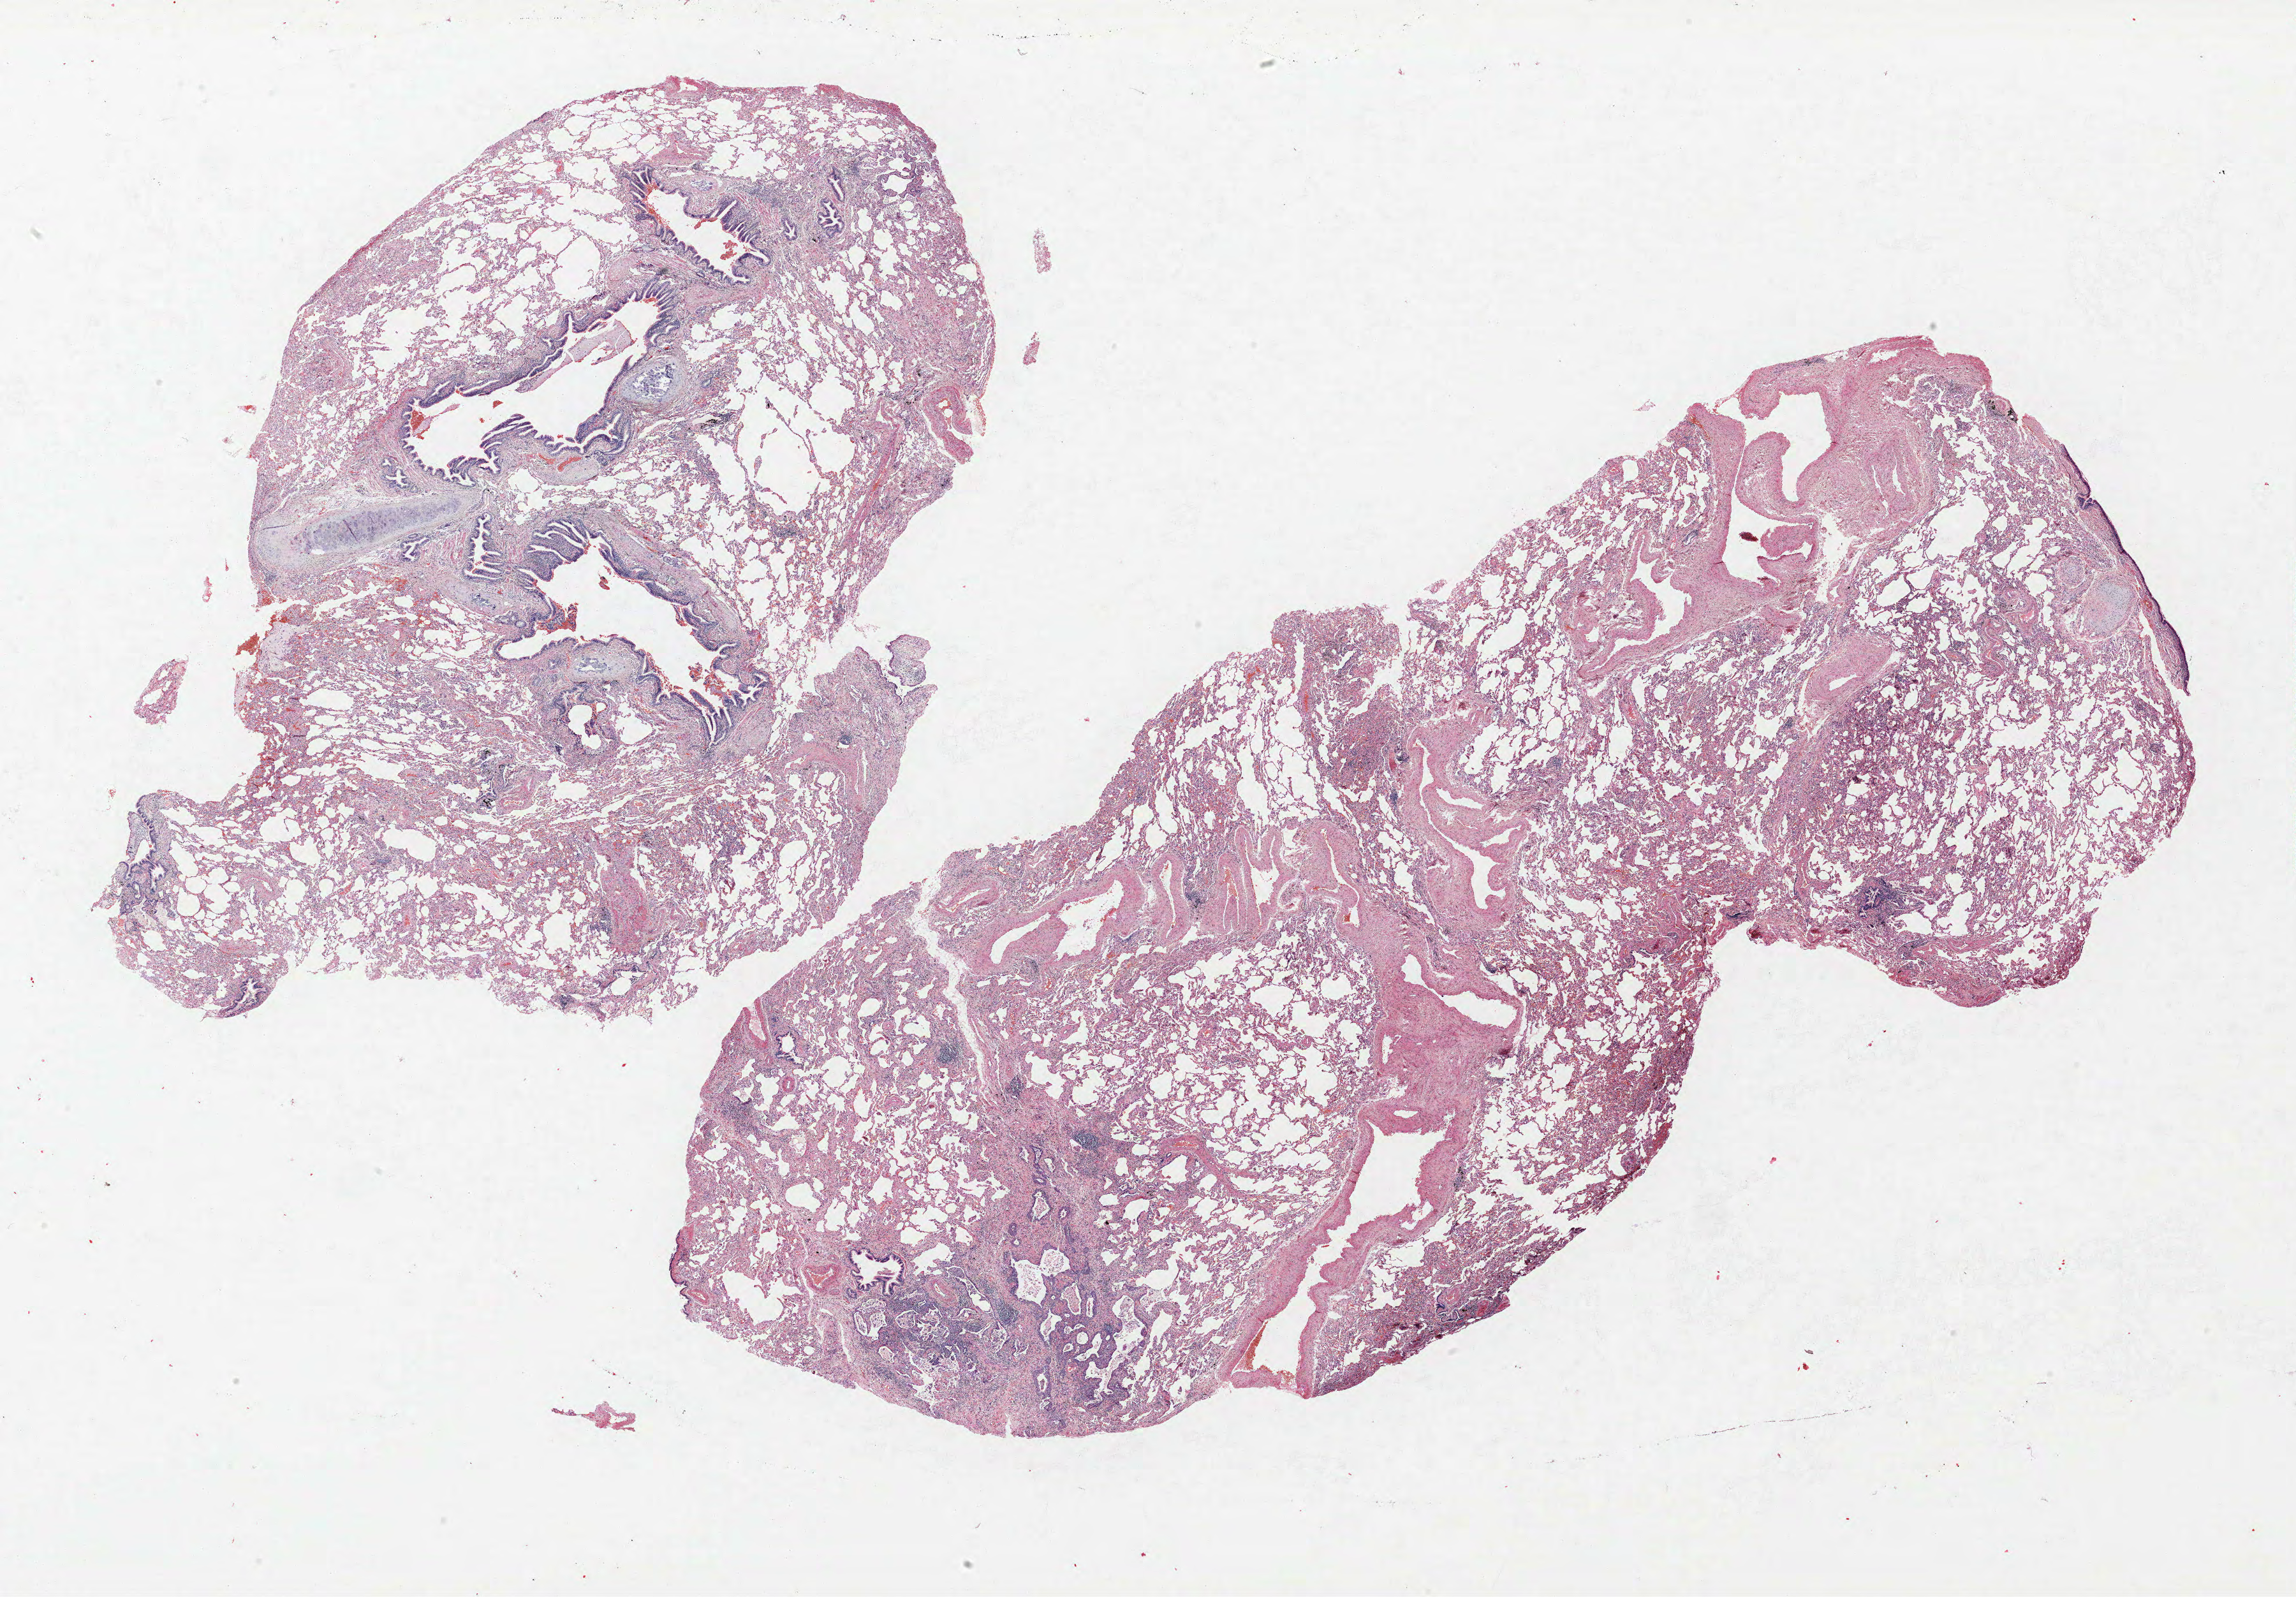
Hematoxylin and eosin (H&E) stained whole-slide image, whole scanned area (about 28.8 x 20.0 mm) shown as a low-resolution overview, FFPE section, lung tissue. Female patient, aged 68 at enrolment. Former smoker at enrolment. Grade: poorly differentiated (G3).
- ICD-O-3 topography: lower lobe of lung (C34.3)
- primary tumour location (clinical record): right lower lobe
- tumour size (pathology): 32 mm
- participant's lung-cancer diagnosis: Large cell carcinoma, NOS
- stage (AJCC 6th edition): IB